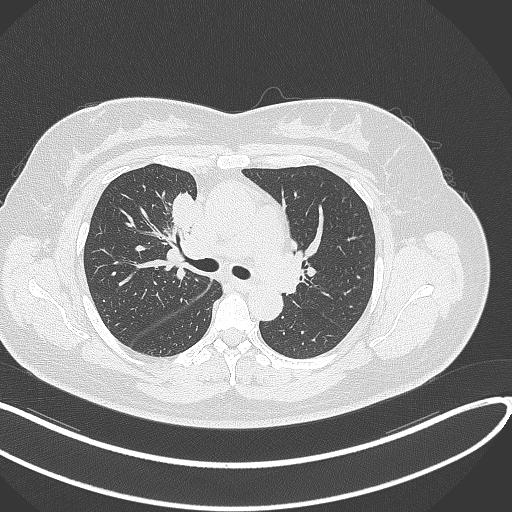
Chest CT, one axial slice. Slice 176 of 303 in the series (ordered by position). Reconstruction kernel B70f. 120 kVp. Lung window (W 1500 / L -600 HU). 1 mm slice thickness. 512 × 512 image matrix, field of view 400 × 400 mm. Female patient, age 46 years. Case-level facts recorded for this patient, not image findings: clinical TNM (as recorded): T2a N1 M0.
Structures marked on this image (rectangle marked by the reading radiologist):
- lung tumour (recorded histology: adenocarcinoma): bounding box <166,189,201,236> (left, top, right, bottom; pixels)